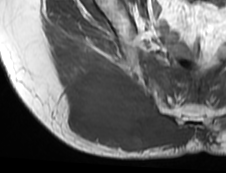
MRI of an extremity soft-tissue mass, one axial slice. MR volume resampled by the dataset authors to the PET/CT grid (not the native acquisition matrix). 3.27 mm slice thickness. 226 × 173 image matrix, field of view 221 × 169 mm. Female patient. Case-level facts recorded for this patient, not image findings: histological type: spindle cell suggestive of myxofibrosarcoma; grade: intermediate; site of the primary tumour: right buttock.
Structures marked on this image (expert contour drawn on MRI and transferred to this co-registered scan by the dataset authors):
- gross tumour volume (mass): bounding box <63,67,188,153> (left, top, right, bottom; pixels)